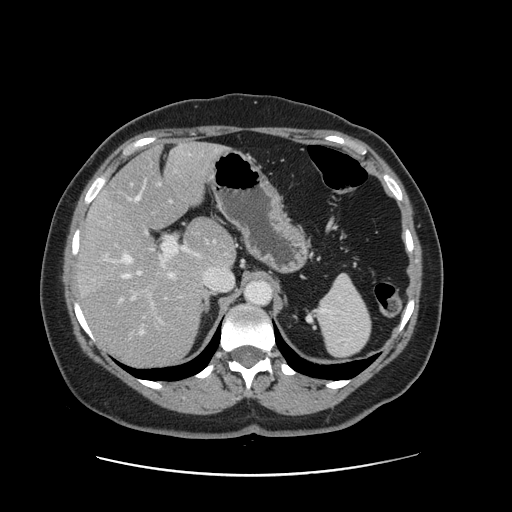
Contrast-enhanced abdominal CT, one axial slice; position 96 of 161 along the scan axis; intravenous contrast given; soft-tissue window (W 400 / L 40 HU); 2.5 mm slice thickness; 512 × 512 image matrix, field of view 398 × 398 mm. Female patient, age 62 years. Case-level facts recorded for this patient, not image findings: diagnosis: colorectal cancer liver metastases, imaged before liver resection; multiple liver metastases: no; largest metastasis: 2.5 cm; disease in both lobes: no.
Structures marked on this image (expert manual segmentation):
- hepatic veins: bounding box (x1, y1, x2, y2) in pixels: (120, 184, 232, 333)
- liver: (80, 144, 235, 366)
- planned liver remnant (the part of the liver to remain after resection): (104, 144, 234, 269)
- portal vein (with intrahepatic branches): (129, 235, 187, 339)